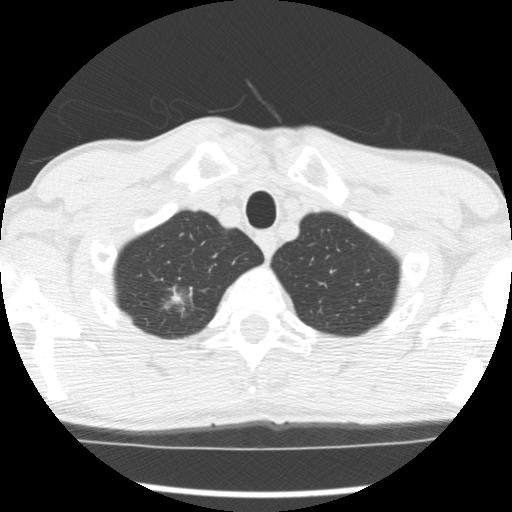
Low-dose screening chest CT, axial slice, first (baseline) screen, lung window (W 1500 / L -600 HU), standard (soft-tissue) reconstruction kernel (STANDARD), slice 27 of 277 in the series, 512 × 512 image matrix. Male, age 66 years at enrolment. Former smoker at enrolment.
Expert-annotated lung lesion, bounding box (x1, y1, x2, y2) in pixels: (155, 282, 202, 327). The screening reader recorded 4 non-calcified nodules or masses ≥4 mm on this exam (right upper lobe, right upper lobe, right upper lobe, left lower lobe); which of them this box marks is not recorded. Official screen result: positive, change unspecified: nodule(s) >= 4 mm or enlarging nodule(s), mass(es), or other non-specific abnormalities suspicious for lung cancer. Participant outcome: lung cancer diagnosed 503 days after this screen (after the second annual screen) — adenocarcinoma, NOS, right upper lobe, undifferentiated (G4), stage IA (AJCC 6th edition), 20 mm at pathology.